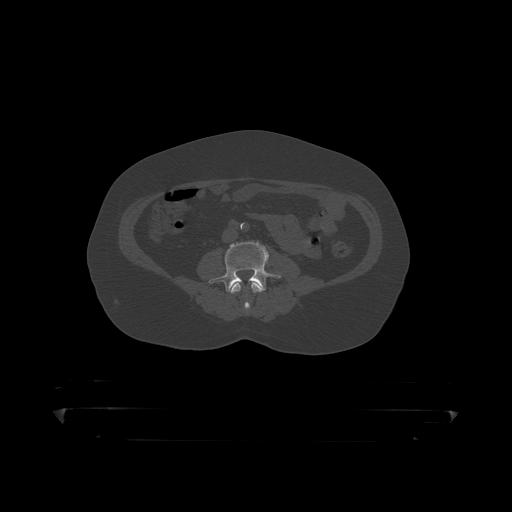
CT including the spine, one axial slice. Position 72 of 390 along the scan axis. Reconstruction kernel STANDARD. Bone window (W 1800 / L 400 HU). 1.25 mm slice thickness. 512 × 512 image matrix, field of view 650 × 650 mm. Patient: male, 60 years. Case-level facts recorded for this patient, not image findings: primary cancer: prostate.
Outlined on this slice (semi-automatically segmented with operator editing):
- L3 vertebra: bounding box <230,282,264,313> (left, top, right, bottom; pixels)
- L4 vertebra: <209,240,281,293>